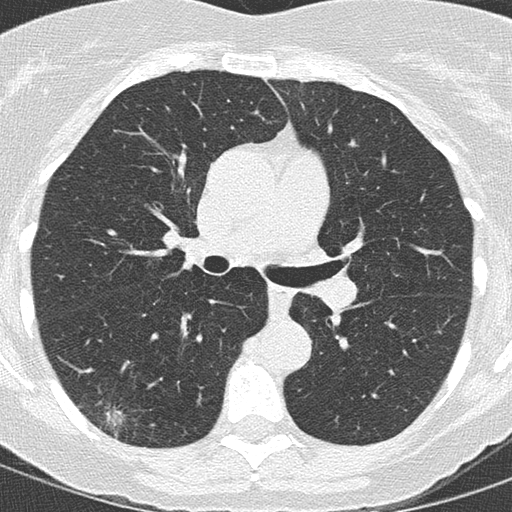
Low-dose screening chest CT, axial slice. Baseline screening round. Lung window (W 1500 / L -600 HU). 2 mm slice thickness. Slice 62 of 146 in the series. 512 × 512 image matrix. Female, age 59 years at enrolment. Former smoker at enrolment.
- Expert-annotated lung lesion, box from (x=68, y=386) to (x=146, y=446) px.
- Reader record for this screening exam (exam-level; its link to the box is not recorded): non-calcified nodule or mass ≥4 mm, right lower lobe, 24 × 15 mm, spiculated (stellate) margins, soft tissue attenuation.
- Official screen result: positive, change unspecified: nodule(s) >= 4 mm or enlarging nodule(s), mass(es), or other non-specific abnormalities suspicious for lung cancer.